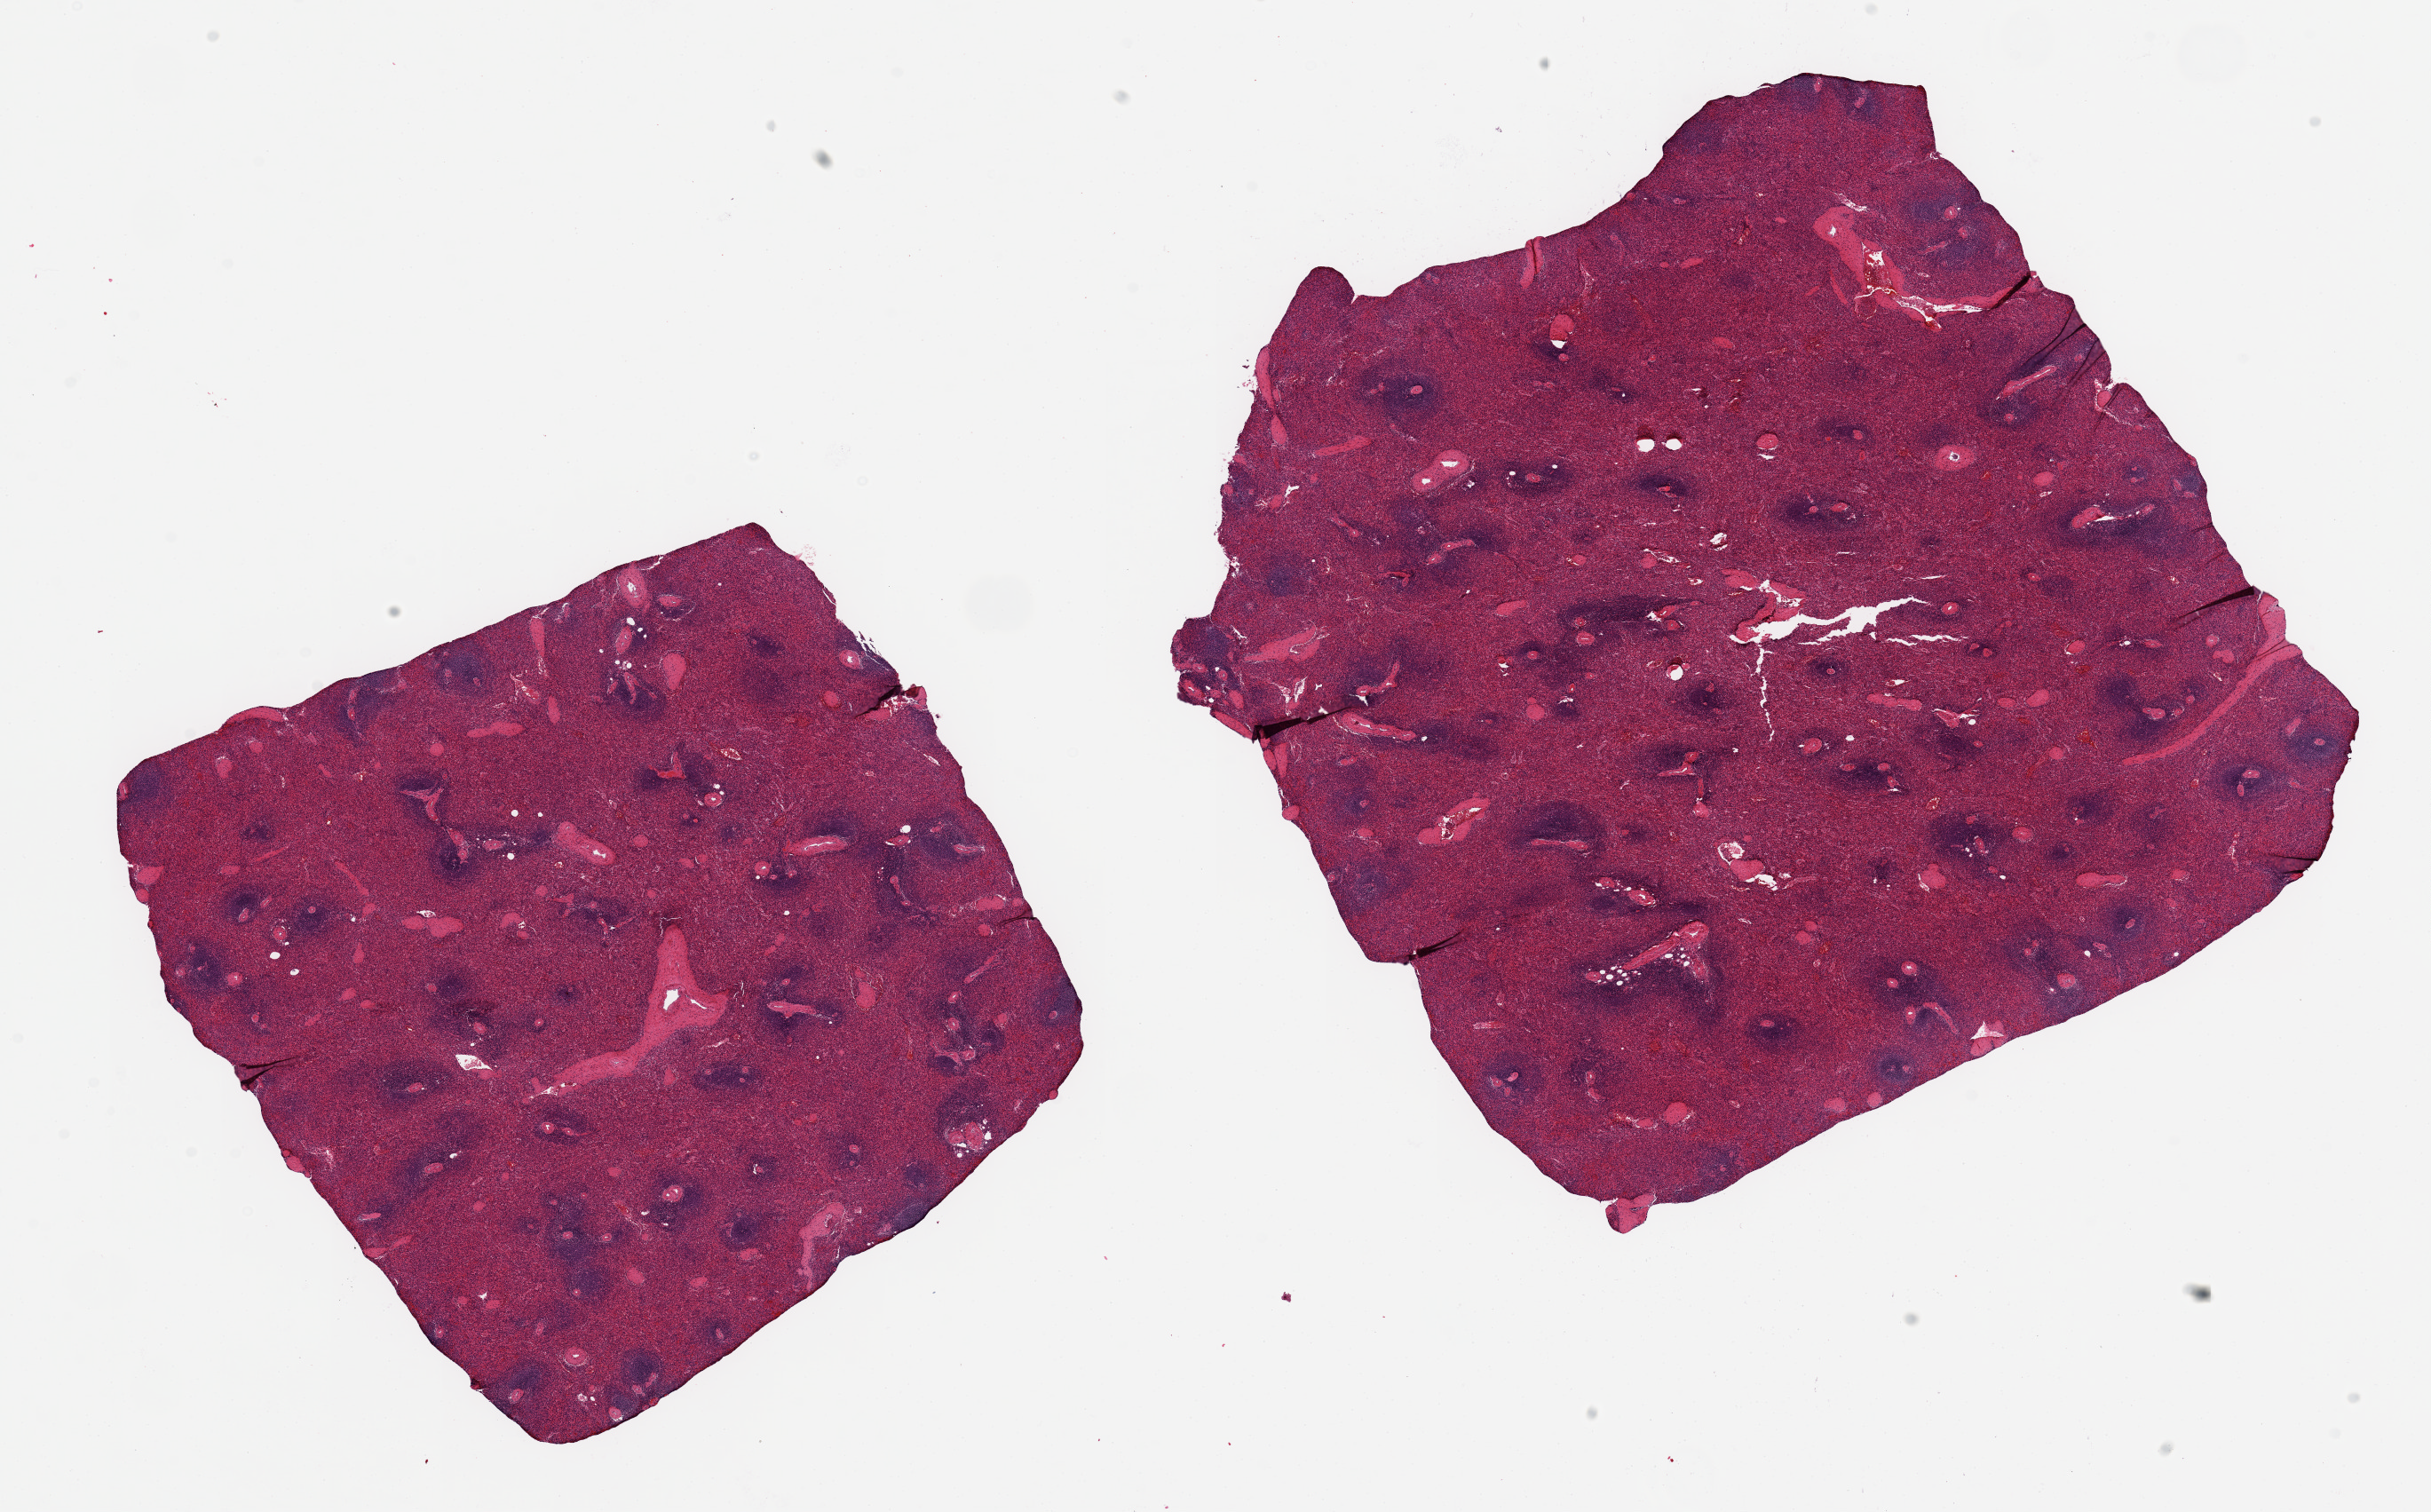
Digitized haematoxylin and eosin-stained section, brightfield, a low-resolution overview of the entire scanned area, about 21.7 x 13.5 mm (slide scanned at 20x). PAXgene-fixed paraffin-embedded (PFPE) section. Sampled site (target tissue): spleen. Tissue donor sample. Donor: female.
• reviewer comment on this tissue sample: 2 pieces 9x8 & 7x7 mm; not congested